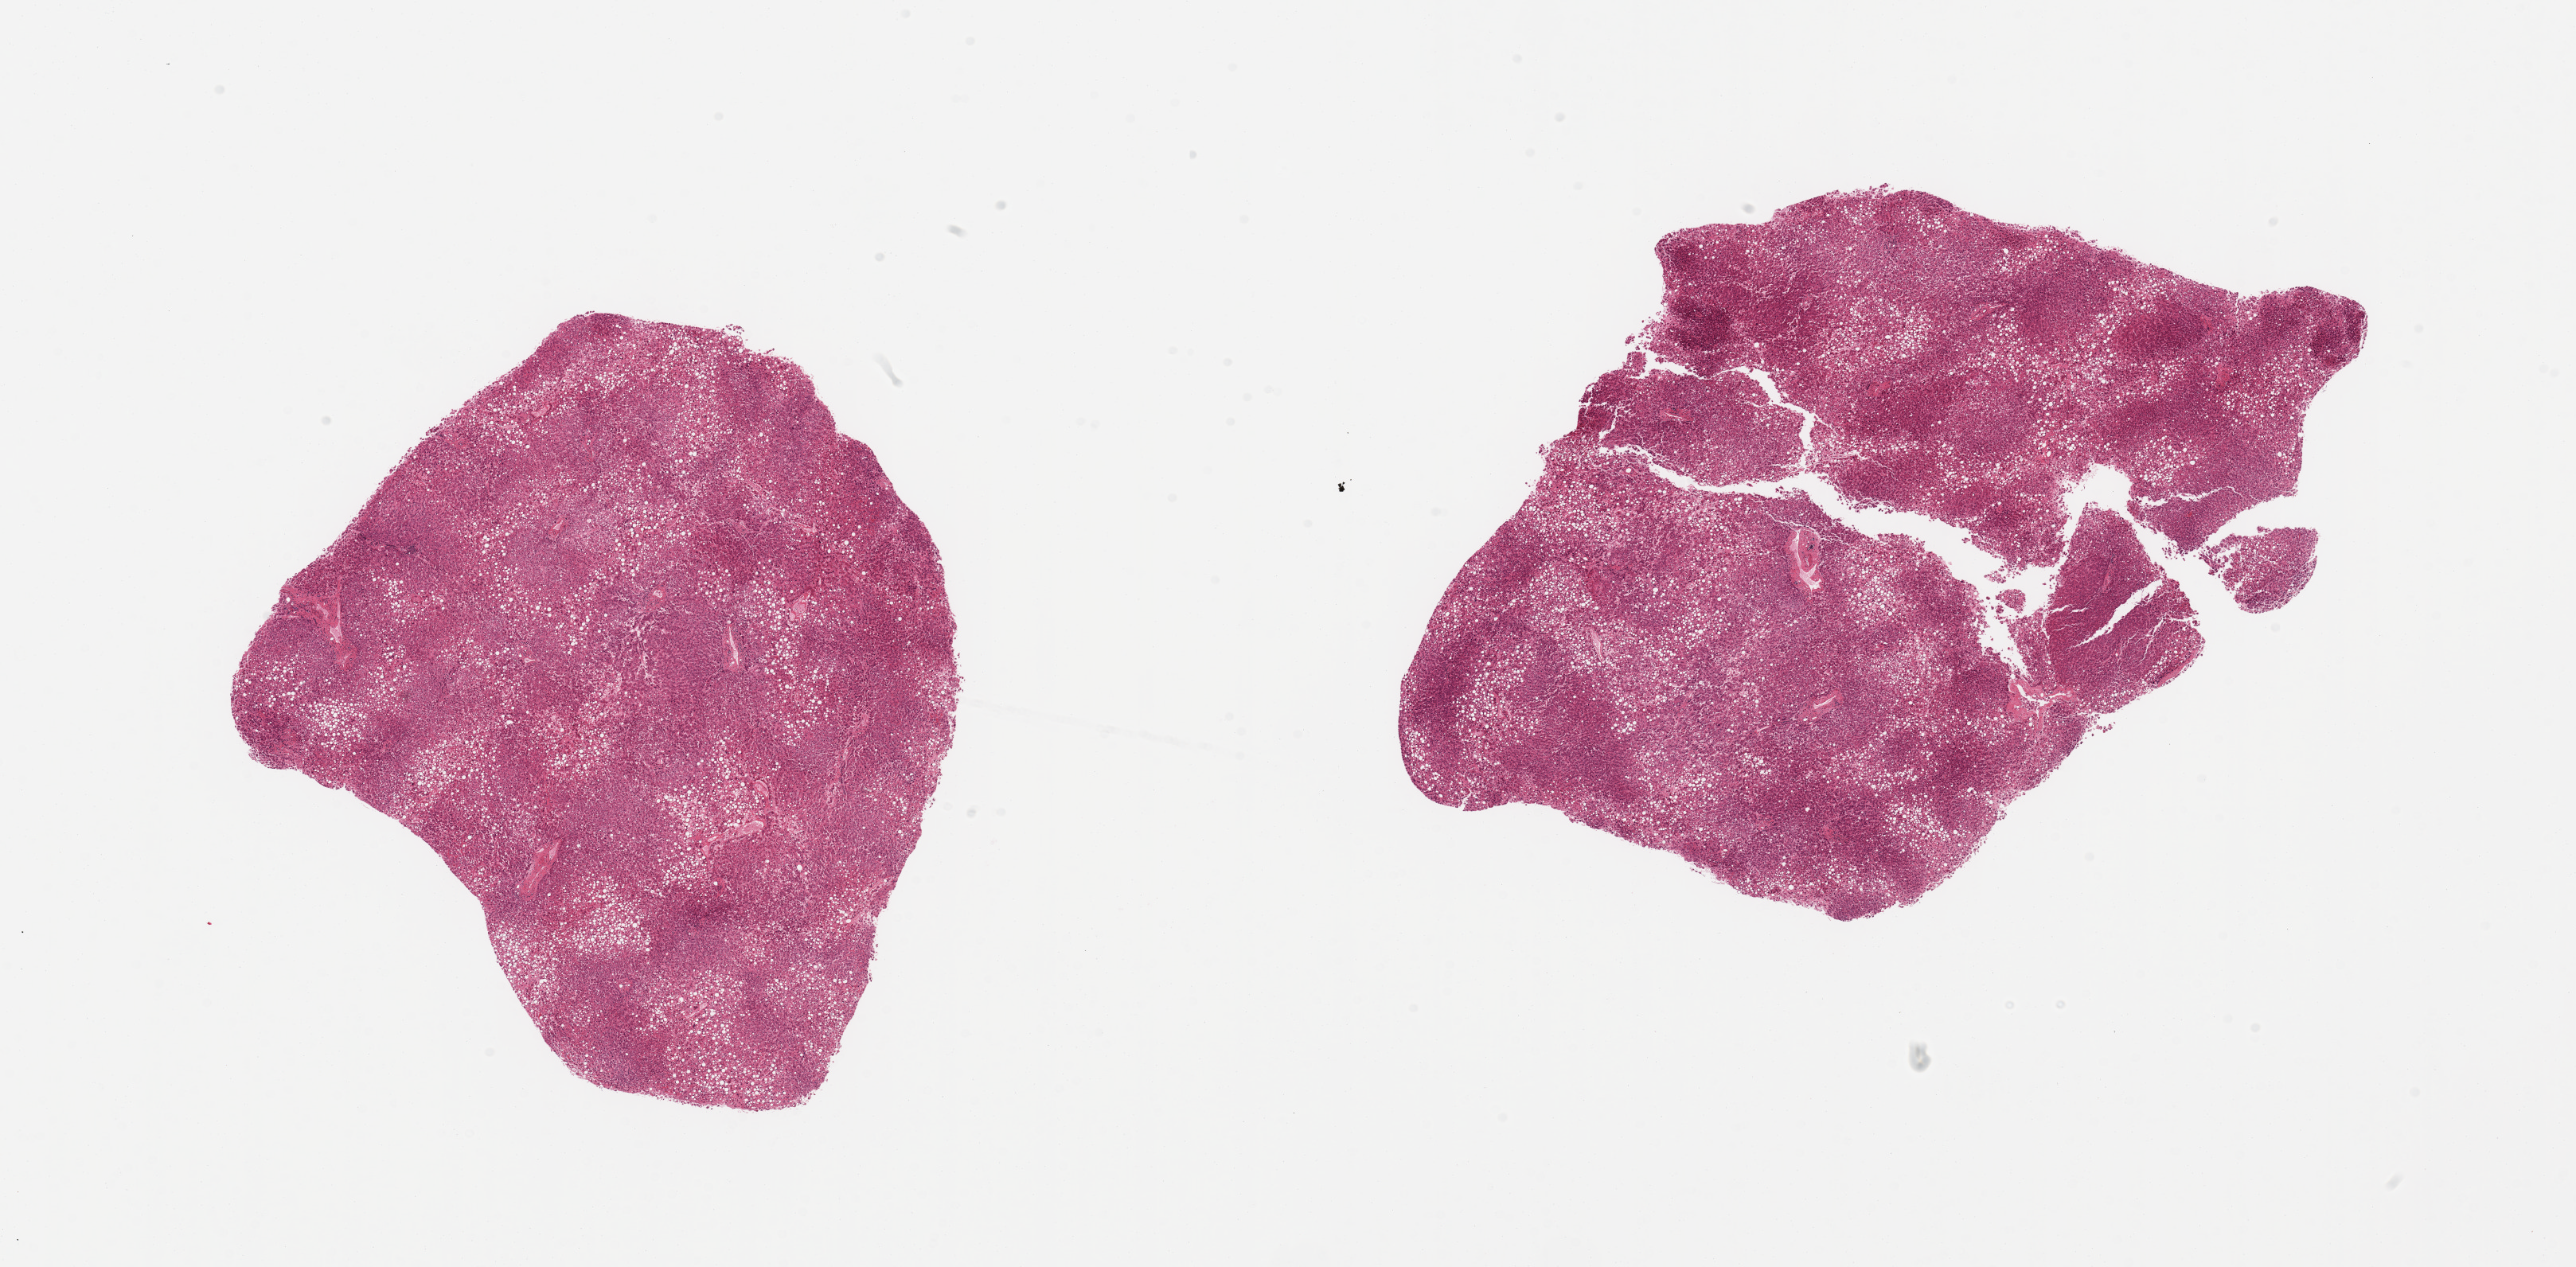
Hematoxylin and eosin (H&E) whole-slide image, brightfield — low-resolution overview of the scanned area, about 25.6 x 12.6 mm (slide scanned at 20x), PAXgene-fixed, paraffin-embedded tissue, section of liver (target tissue), donor tissue sample. Donor sex: male.
Review note (as recorded): 2 pieces; moderate steatosis.